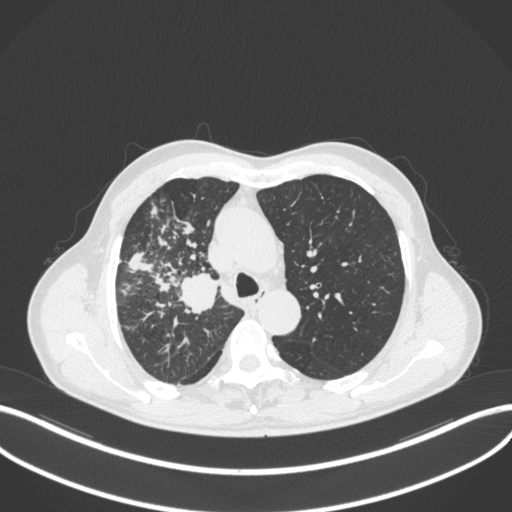
Chest CT, one axial slice; position 341 of 490 along the scan axis; reconstruction kernel B31f; lung window (W 1500 / L -600 HU); 512 × 512 image matrix, field of view 400 × 400 mm. Male patient, age 69 years. From the clinical record (not read from this slice): clinical TNM (as recorded): T2a N0 M0.
Outlined on this slice (bounding box drawn by a radiologist):
- lung tumour (recorded histology: adenocarcinoma): box from (x=173, y=272) to (x=219, y=317) px